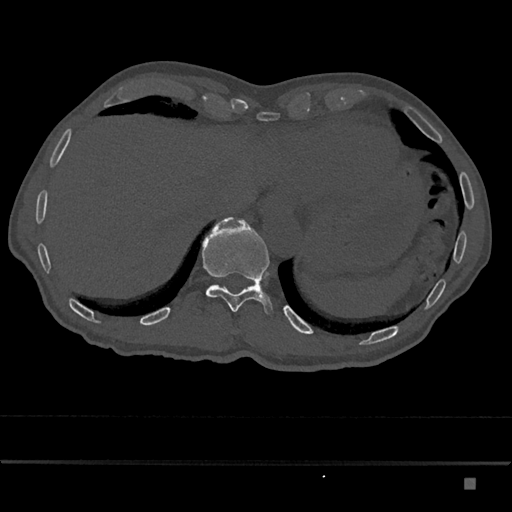
CT including the spine, one axial slice; slice 677 of 797 in the series (ordered by position); 120 kVp; bone window (W 1800 / L 400 HU); 0.5 mm slice thickness; 512 × 512 image matrix, field of view 390 × 390 mm. Male patient, age 72 years. Case-level facts recorded for this patient, not image findings: primary cancer: prostate.
Annotated regions visible in this slice (semi-automatically segmented with operator editing):
- T11 vertebra: box from (x=202, y=217) to (x=274, y=314) px